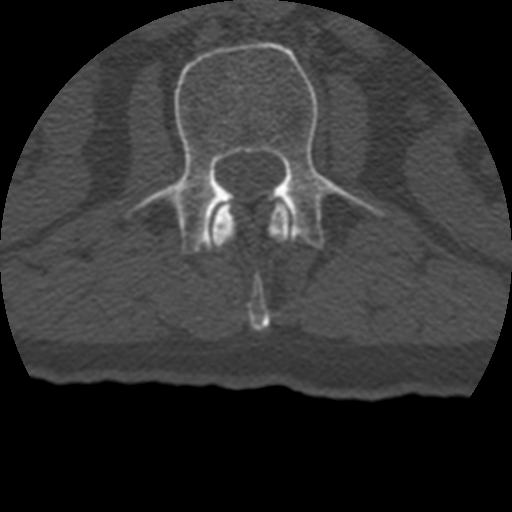
CT including the spine, one axial slice. Slice 124 of 399 in the series (ordered by position). Reconstruction kernel STANDARD. Bone window (W 1800 / L 400 HU). 1.25 mm slice thickness. 512 × 512 image matrix, field of view 160 × 160 mm. Patient age 69 years. Case-level facts recorded for this patient, not image findings: primary cancer: prostate.
Annotated regions visible in this slice (semi-automatic segmentation, software-assisted and operator-edited):
- L1 vertebra: bounding box [x1, y1, x2, y2] px = [211, 199, 293, 331]
- L2 vertebra: [123, 42, 391, 254]